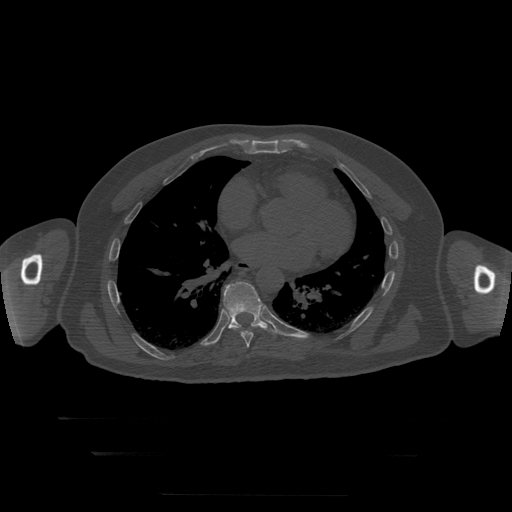
CT including the spine, one axial slice. Position 155 of 397 along the scan axis. Reconstruction kernel STANDARD. 120 kVp. Bone window (W 1800 / L 400 HU). 512 × 512 image matrix, field of view 510 × 510 mm. Patient age 73 years. Case-level facts recorded for this patient, not image findings: primary cancer: prostate.
Annotated regions visible in this slice (semi-automatically segmented with operator editing):
- T8 vertebra: box from (x=226, y=311) to (x=254, y=348) px
- T9 vertebra: (x=223, y=282)–(x=275, y=334)